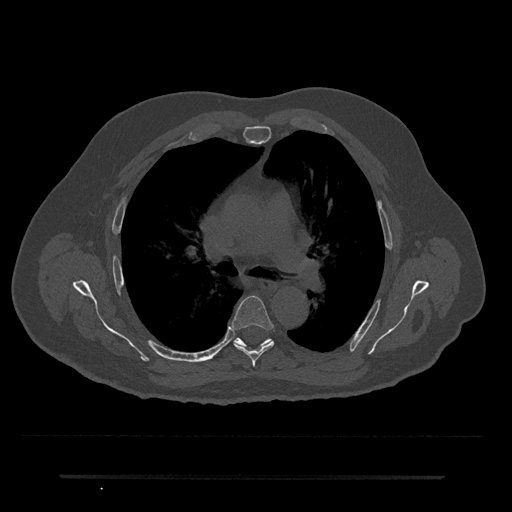
CT including the spine, one axial slice; position 469 of 797 along the scan axis; bone window (W 1800 / L 400 HU); 0.5 mm slice thickness; 512 × 512 image matrix, field of view 437 × 437 mm. Male patient, age 69 years. Case-level facts recorded for this patient, not image findings: primary cancer: prostate.
Structures marked on this image (semi-automatic segmentation, software-assisted and operator-edited):
- T5 vertebra: box from (x=231, y=295) to (x=274, y=366) px
- T6 vertebra: (x=235, y=338)–(x=243, y=346)